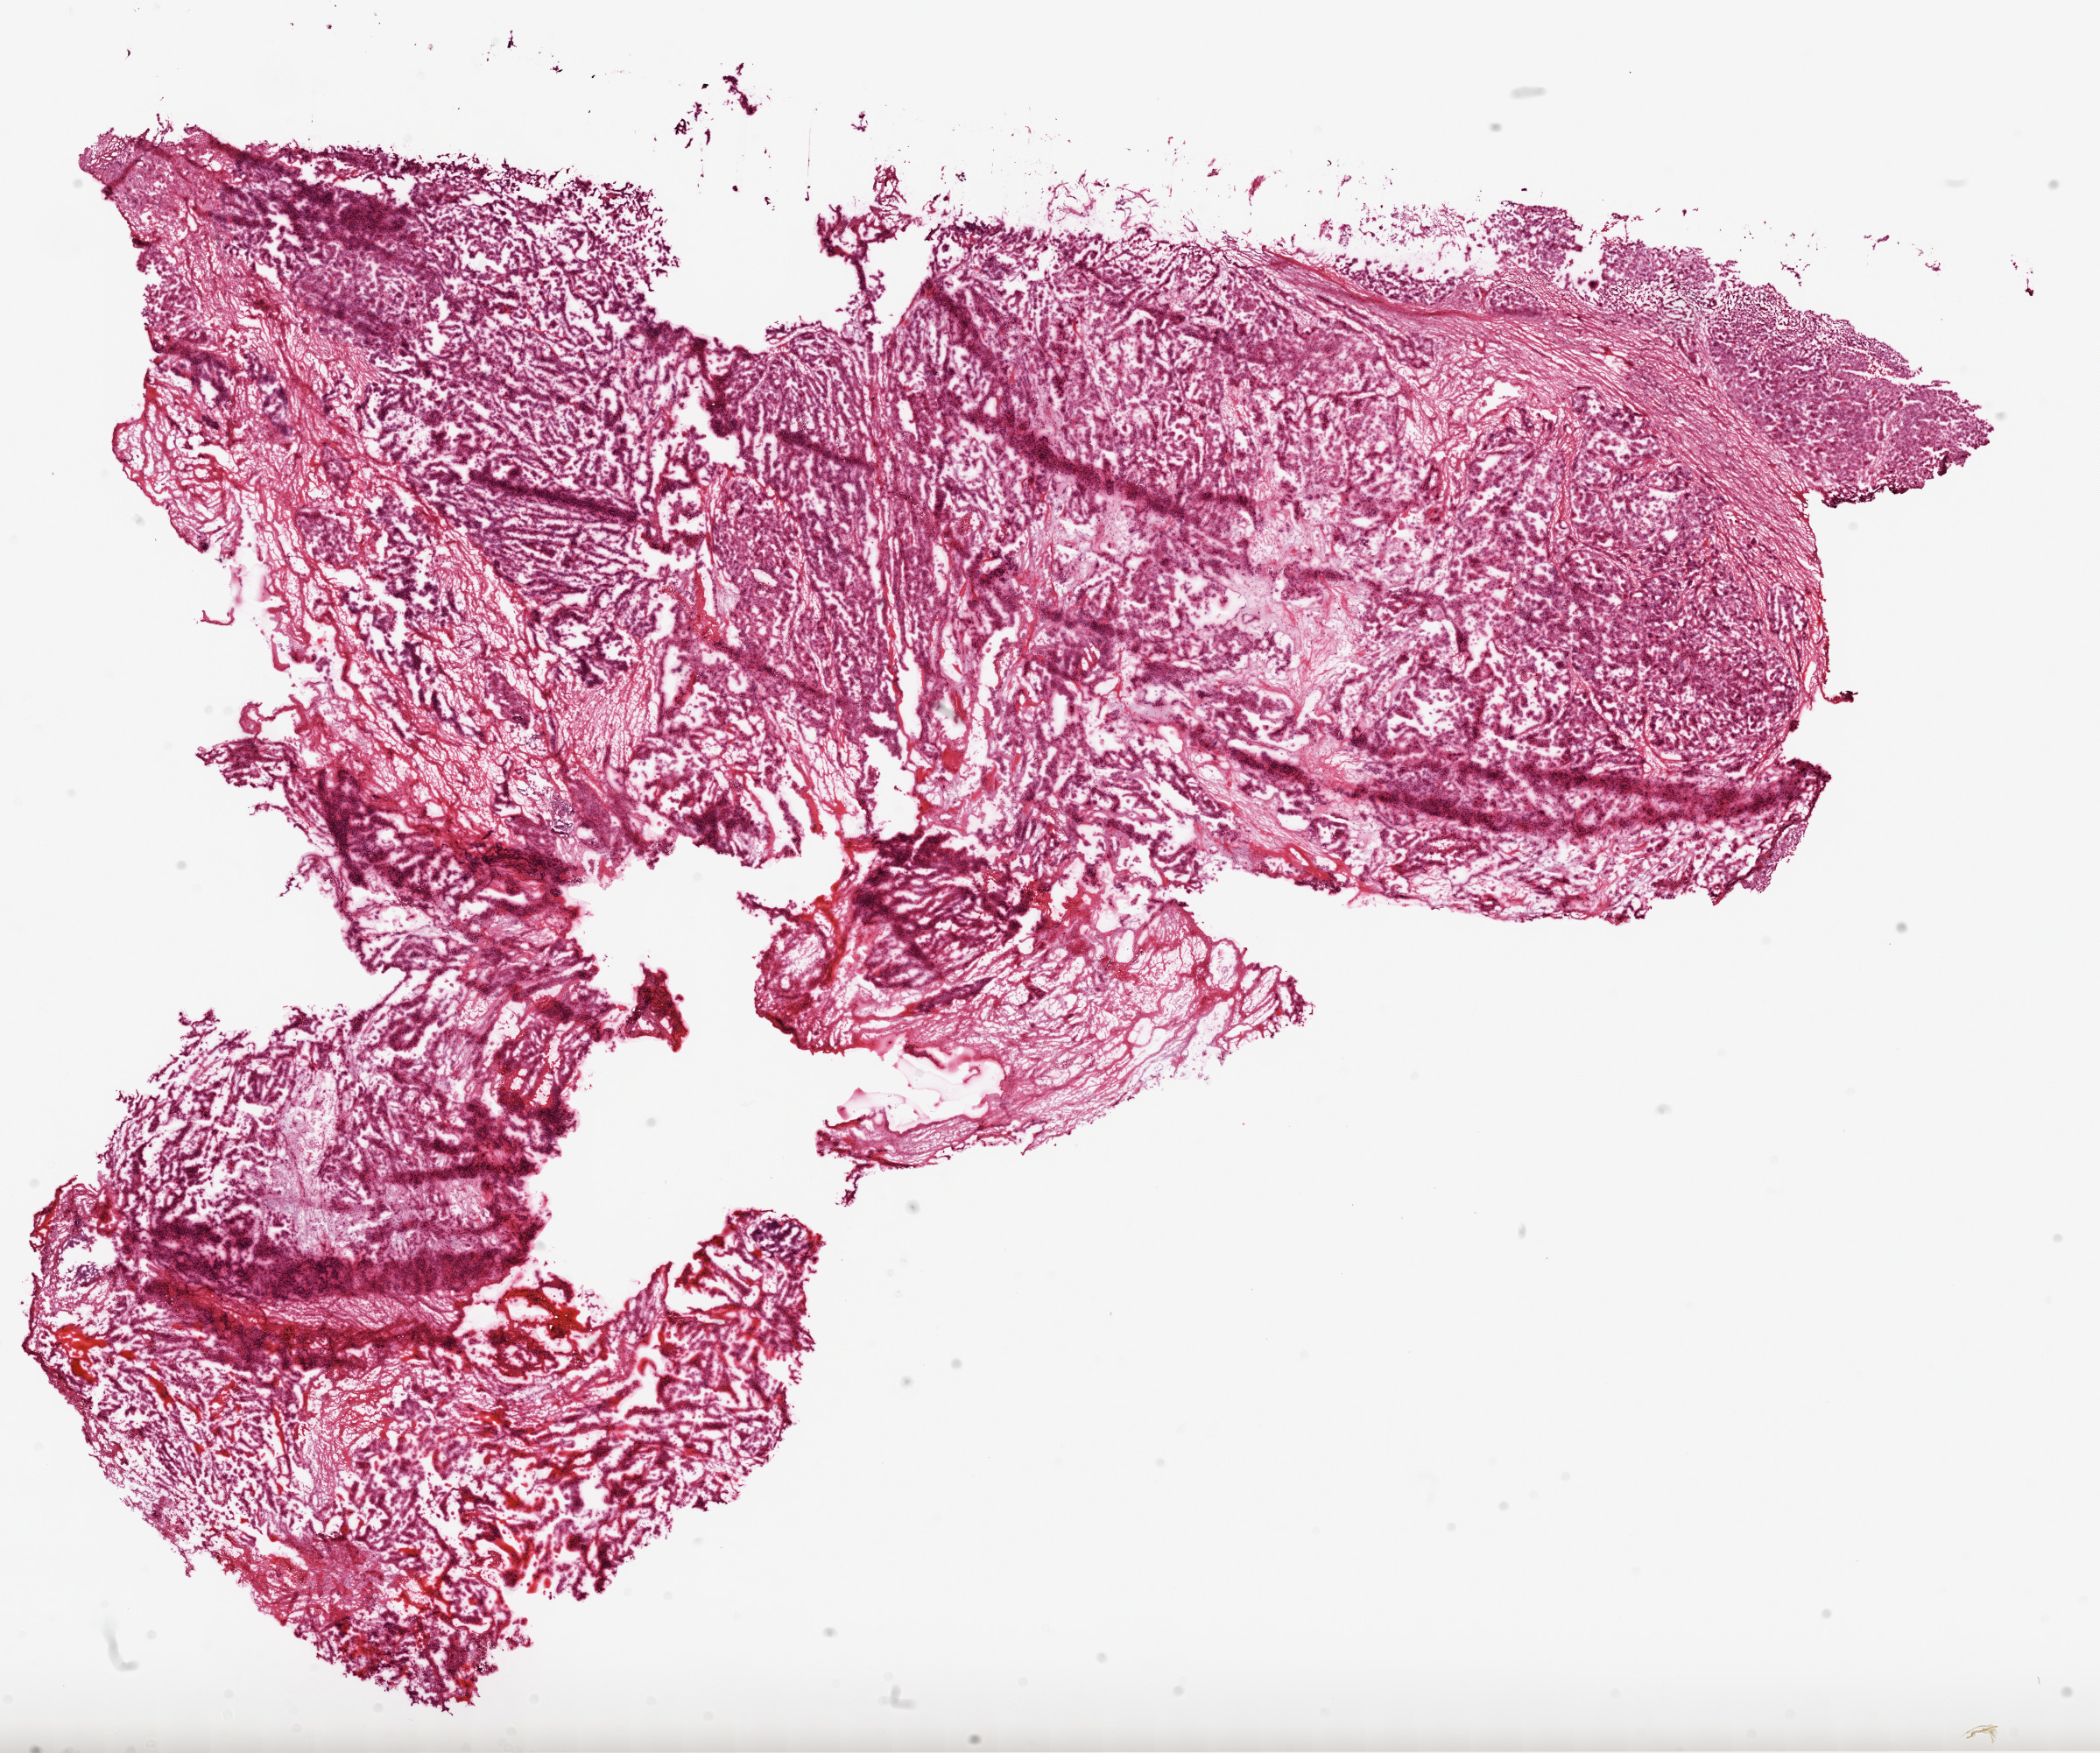
Whole-slide histology image, H&E — low-resolution overview of the scanned area, about 19.3 x 16.1 mm (slide scanned at 20x), frozen section from the top of the tissue portion, sample: primary tumour, ovary. Female patient; age at initial diagnosis 54 years.
Histologic diagnosis: Serous cystadenocarcinoma, NOS.